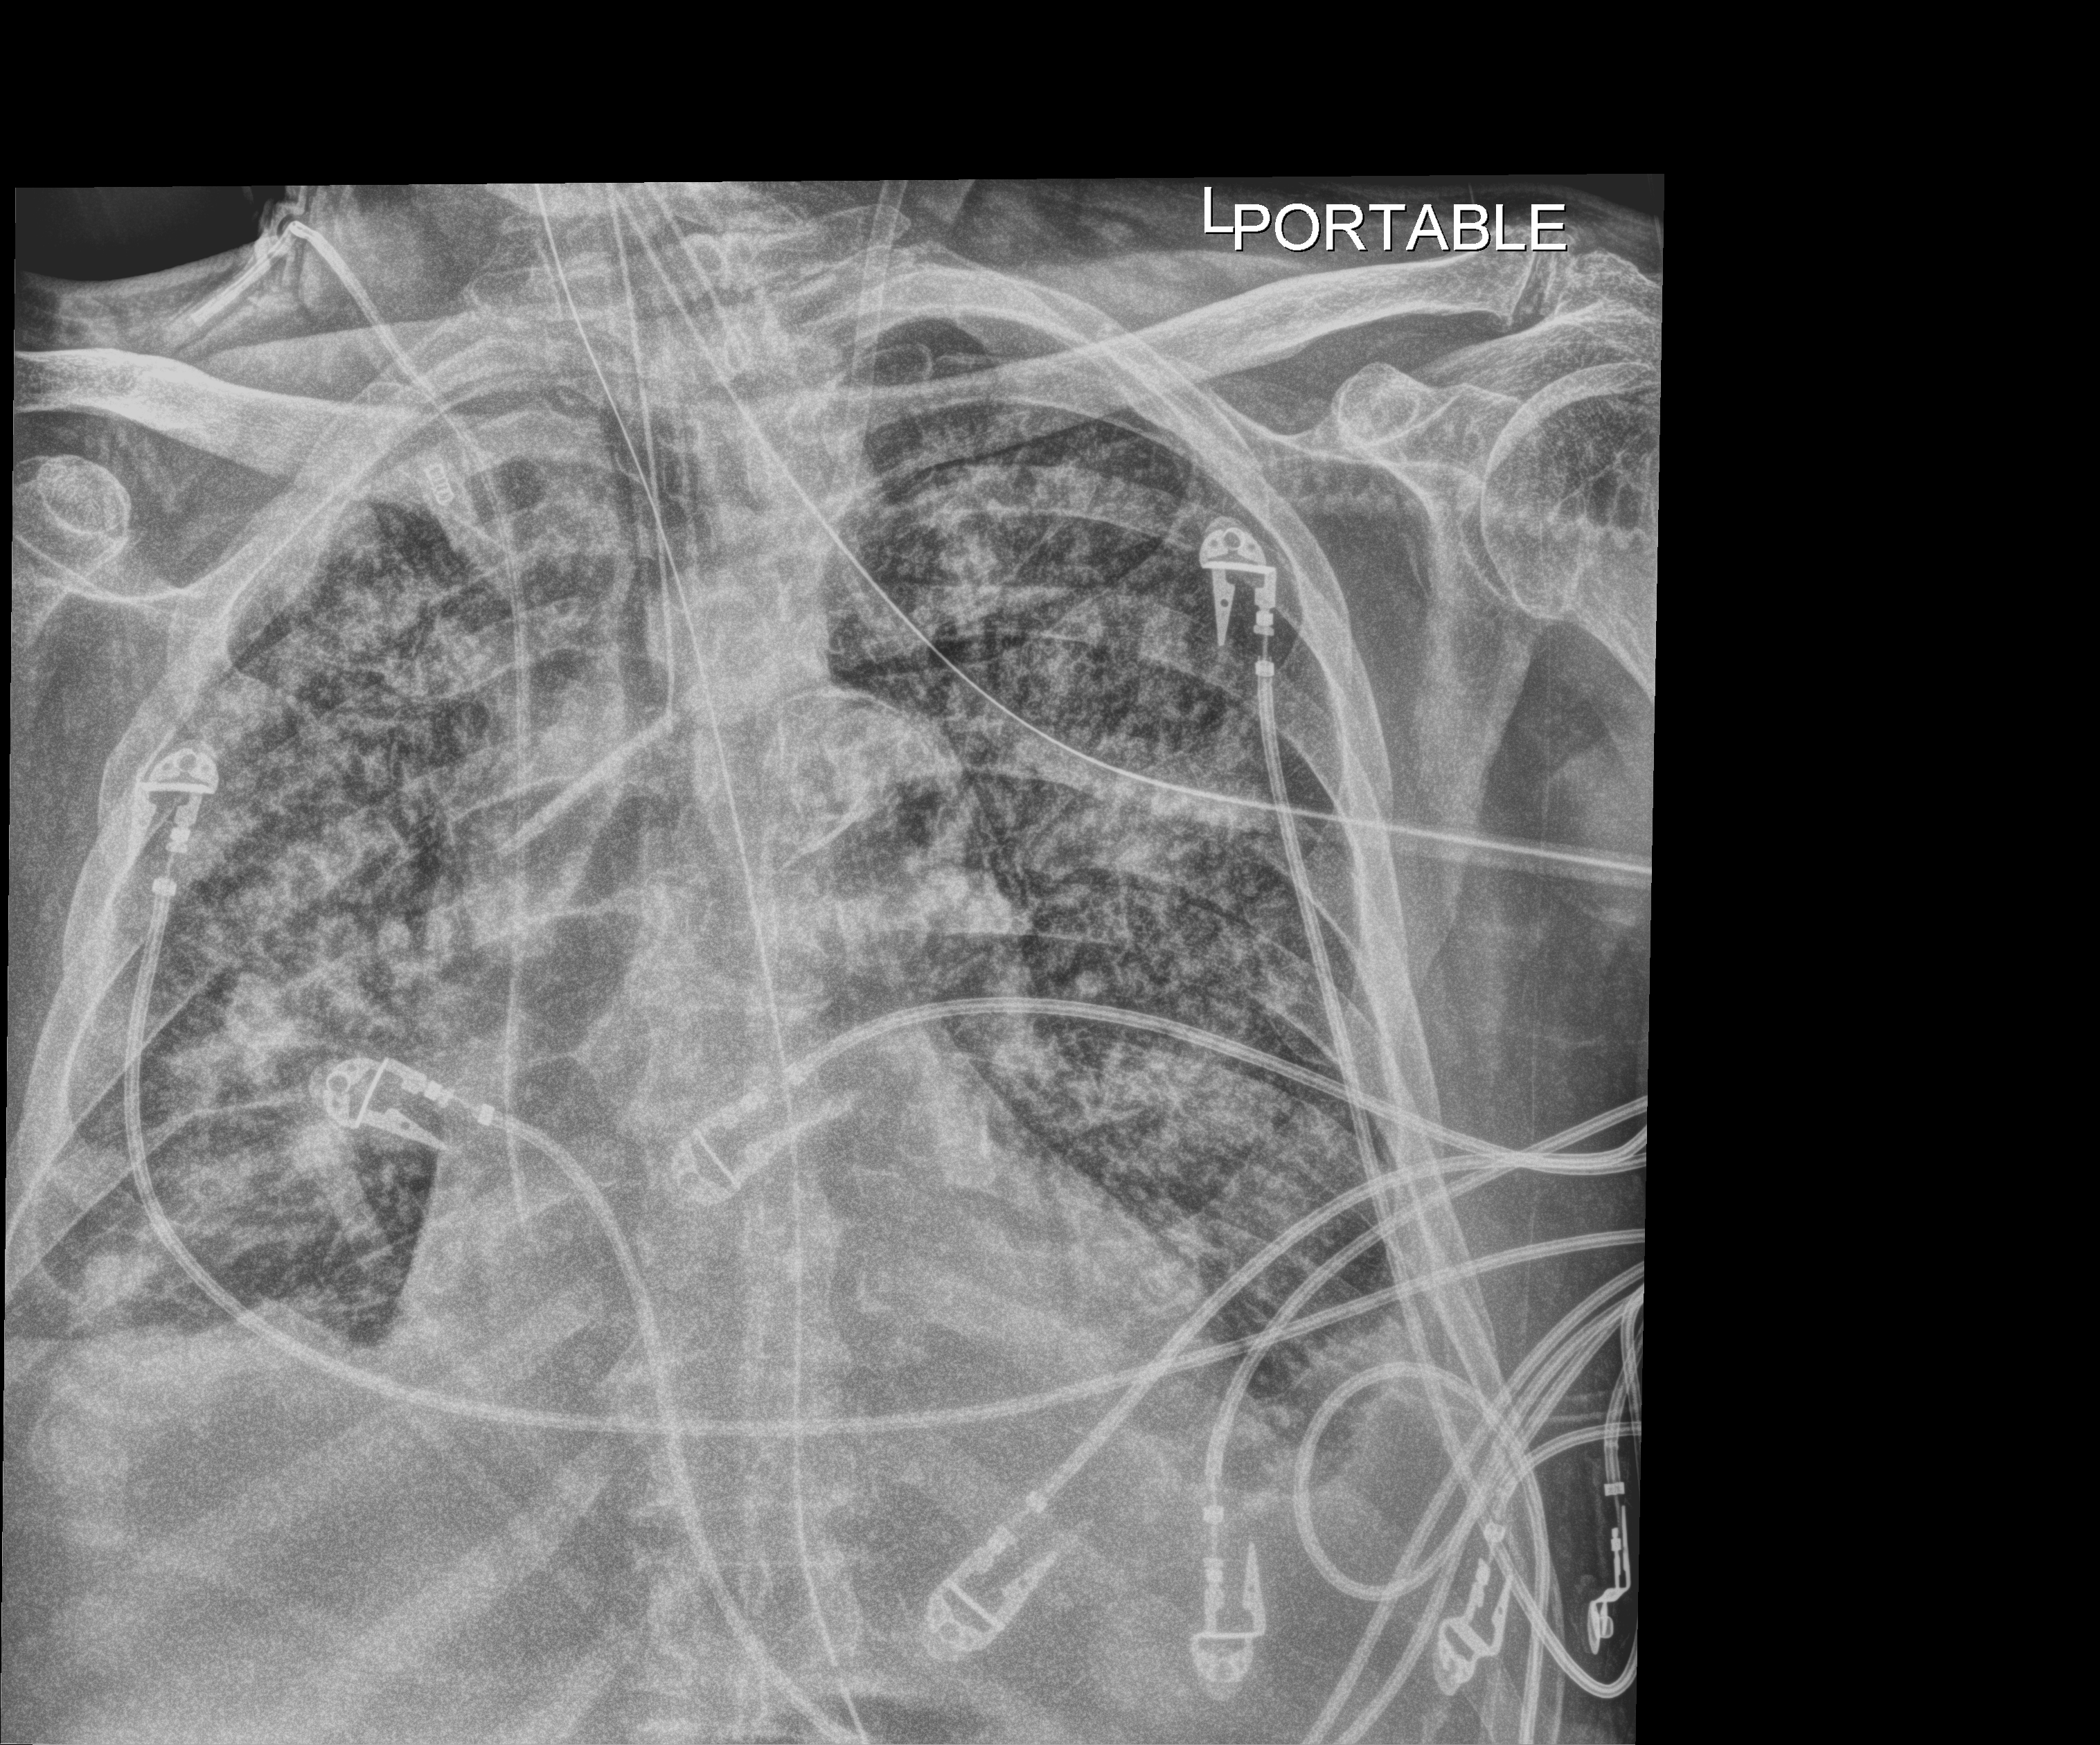
Bedside chest radiograph (digital radiography); anteroposterior (AP) projection. Patient hospitalised with COVID-19; male, aged 75–90 years.
From the hospital-stay record, not from the radiograph (when in the stay this image was taken is not recorded):
- smoking status (admission record): never
- length of hospital stay: 28 days